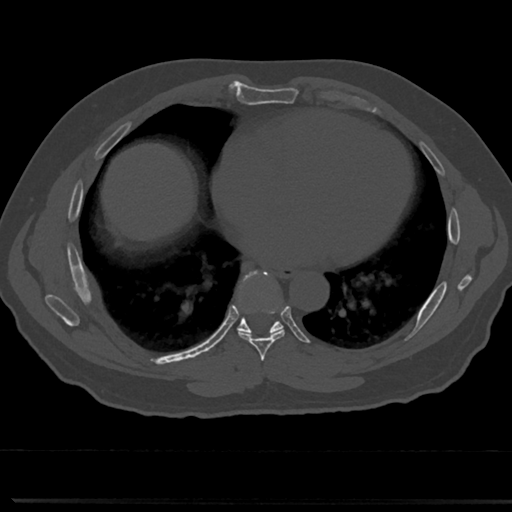
CT including the spine, one axial slice. Reconstruction kernel Br40s/3. 120 kVp. Bone window (W 1800 / L 400 HU). 0.5 mm slice thickness. 512 × 512 image matrix, field of view 355 × 355 mm. Patient: male, 61 years. Case-level facts recorded for this patient, not image findings: primary cancer: prostate.
Structures marked on this image (semi-automatic segmentation, software-assisted and operator-edited):
- T6 vertebra: bounding box [x1, y1, x2, y2] px = [260, 366, 268, 377]
- T7 vertebra: [226, 274, 309, 354]